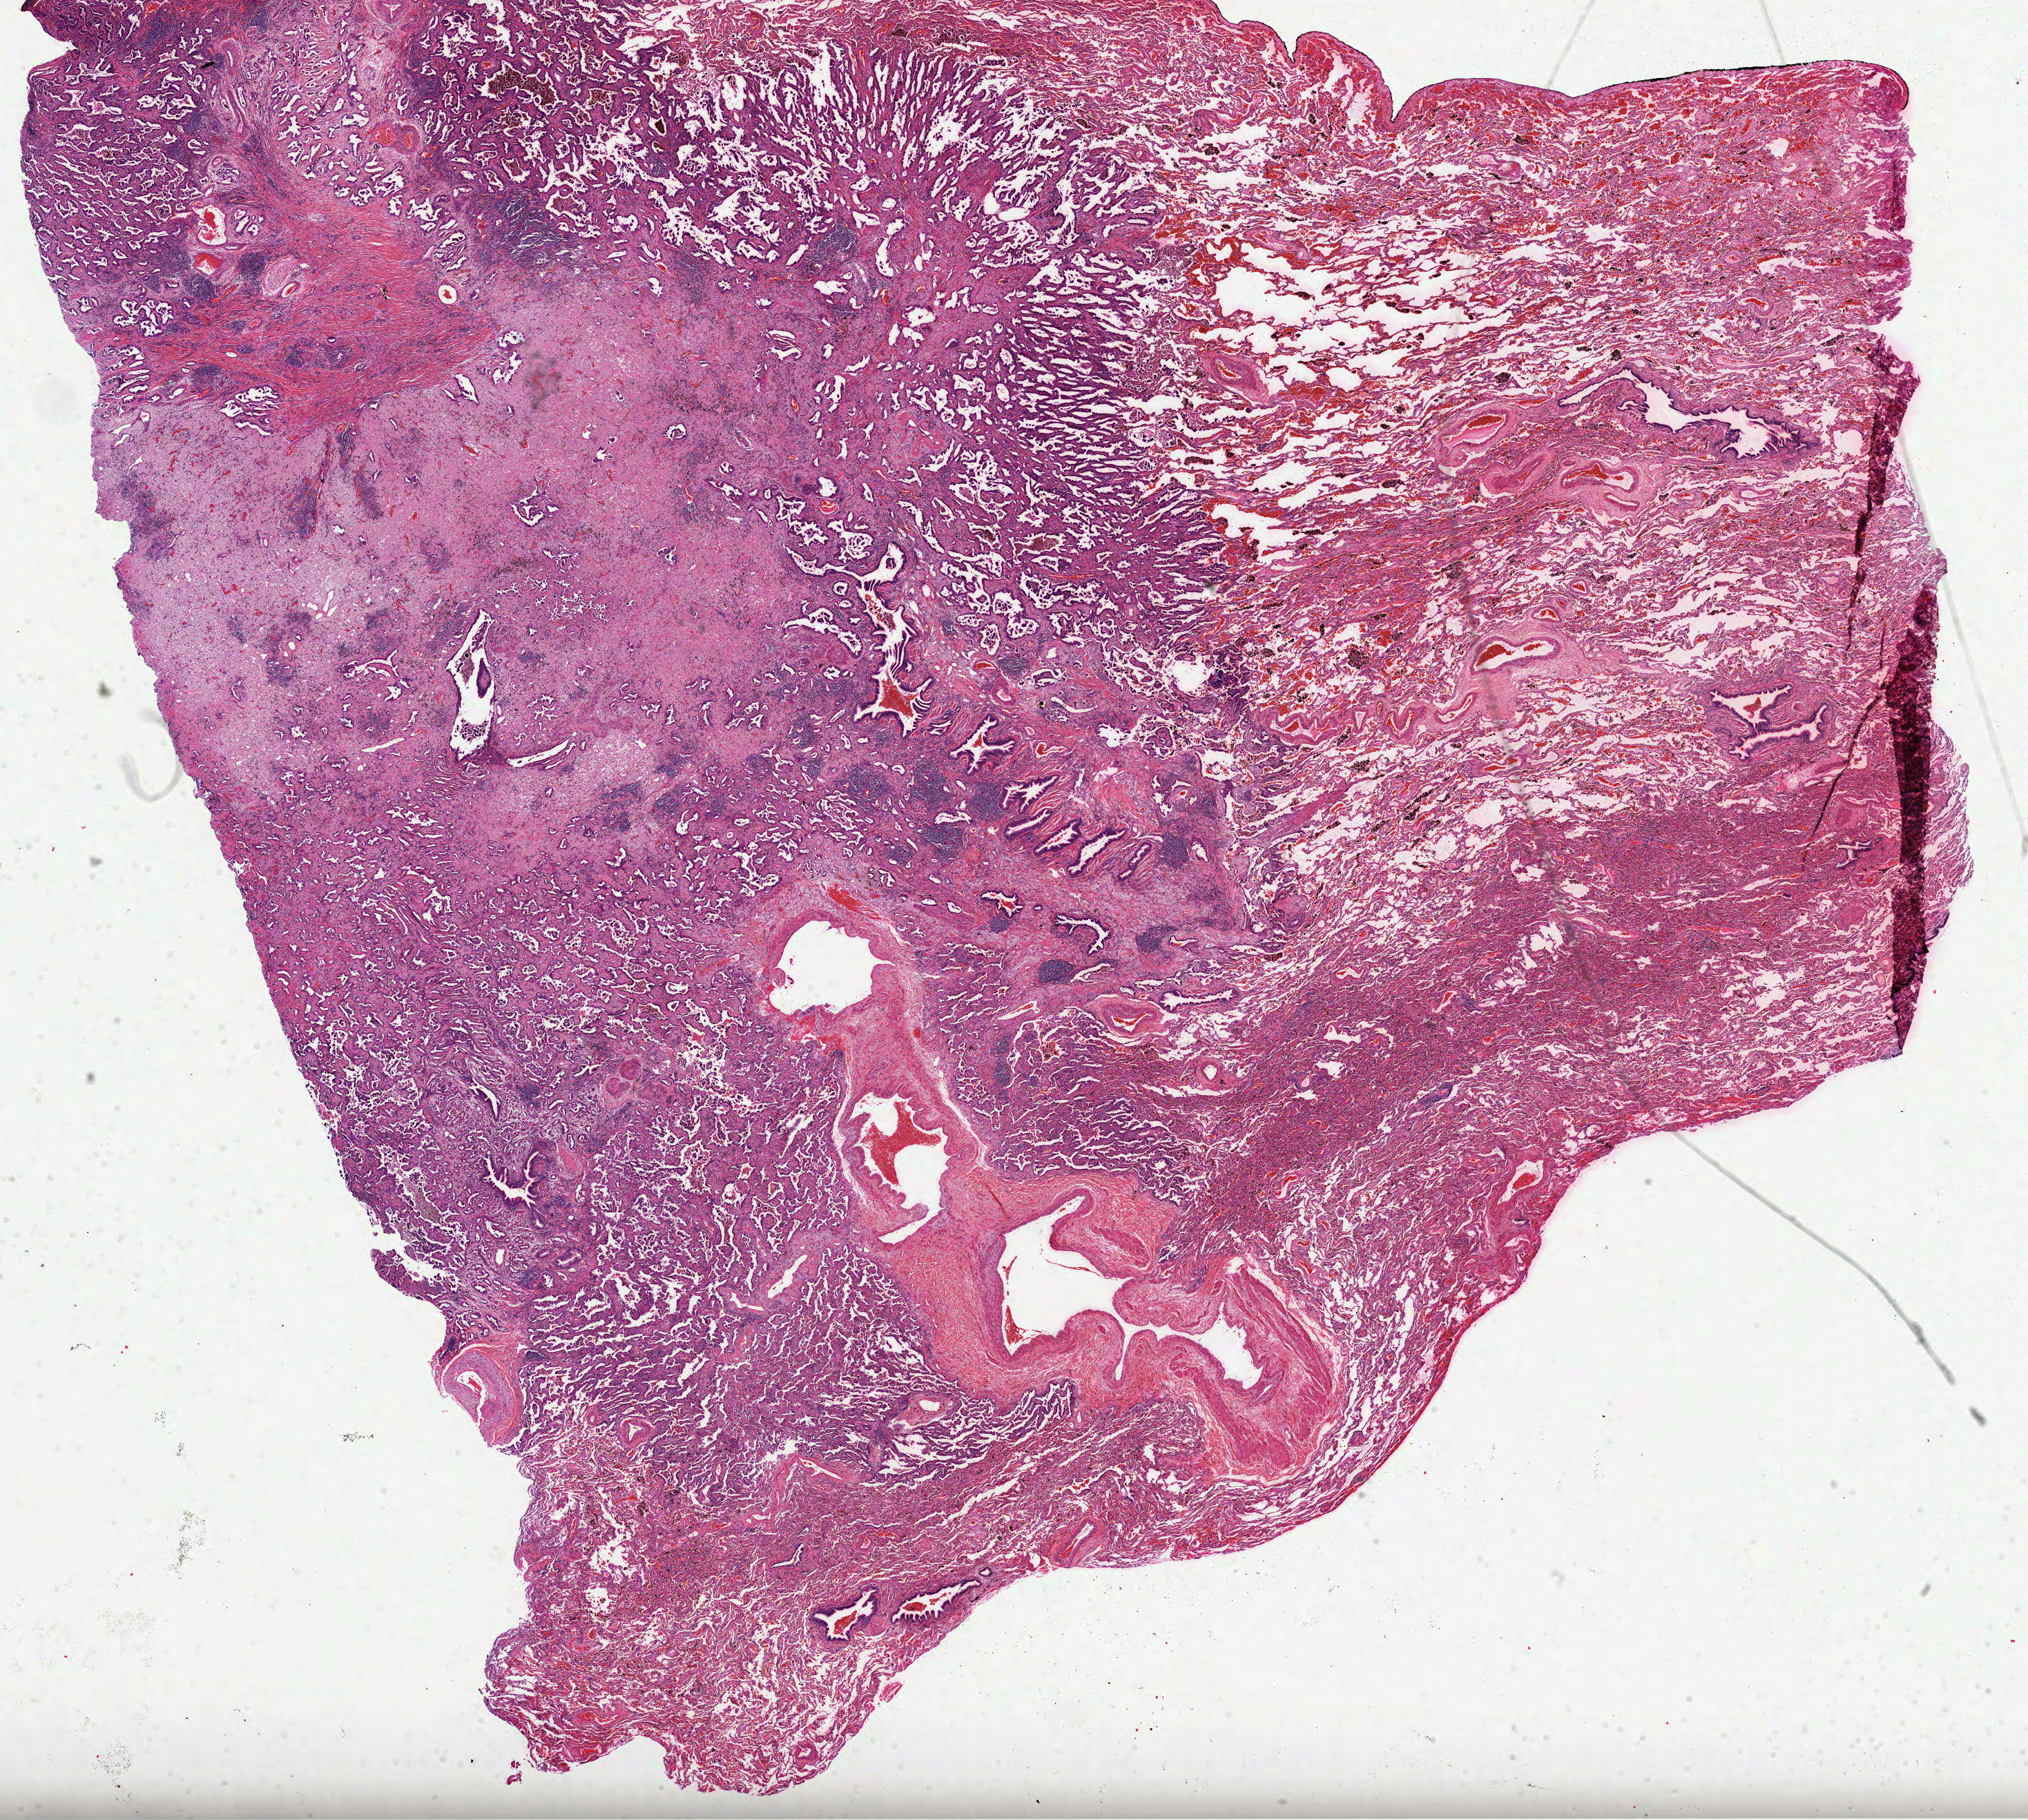
Whole-slide histology image, H&E — whole scanned area (about 23.7 x 21.3 mm) shown as a low-resolution overview; formalin-fixed paraffin-embedded (FFPE) diagnostic section; primary tumour sample from the lung. Female, age 67 years at initial diagnosis.
- AJCC pathologic stage: IB
- TNM: T2 N0 M0
- pathologic diagnosis: Adenocarcinoma, NOS (upper lobe, lung)